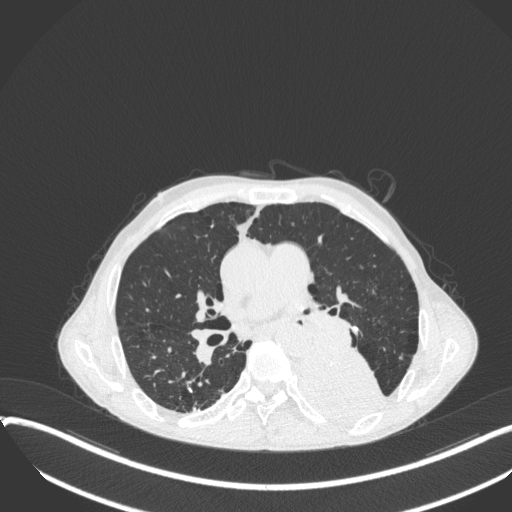
Chest CT, one axial slice; position 207 of 400 along the scan axis; reconstruction kernel B31f; 120 kVp; lung window (W 1500 / L -600 HU); 1 mm slice thickness; 512 × 512 image matrix, field of view 400 × 400 mm. Male patient, age 57 years. Case-level facts recorded for this patient, not image findings: clinical TNM (as recorded): T4 N0 M0.
Outlined on this slice (bounding box drawn by a radiologist):
- lung tumour (recorded histology: squamous cell carcinoma): box from (x=298, y=346) to (x=387, y=431) px